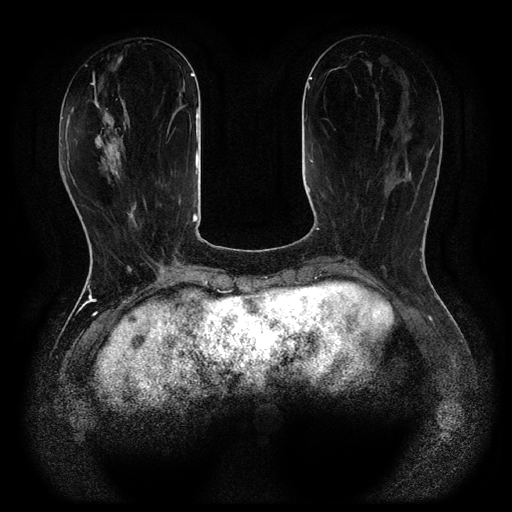
Breast MRI (dynamic contrast-enhanced, multi-phase), one axial slice. Slice 35 of 116 in the series (ordered by position). Dynamic contrast-enhanced series, time point 2 of 5 at this slice position (early post-contrast). 1.5 T. TE 2.6 ms, TR 5.4 ms. 512 × 512 image matrix, field of view 340 × 340 mm. Female patient, age 48 years.
Annotated regions visible in this slice (semi-automatic segmentation, software-assisted and operator-edited):
- breast lesion (labelled benign in the annotation): bounding box [x1, y1, x2, y2] px = [95, 107, 126, 182]